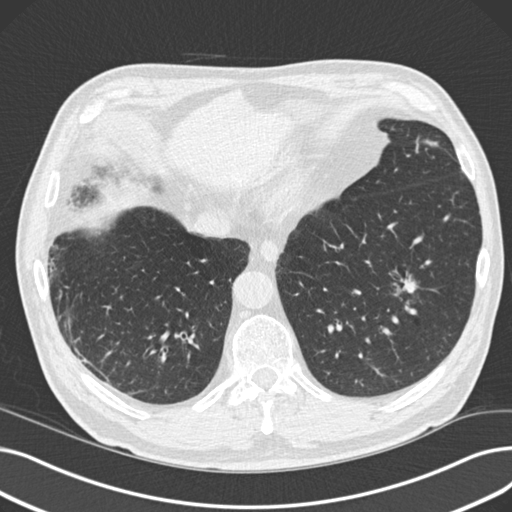
Low-dose screening chest CT, one axial slice; position 37 of 165 along the scan axis; lung window (W 1500 / L -600 HU); 2 mm slice thickness; 512 × 512 image matrix, field of view 369 × 369 mm.
Outlined on this slice (outlined manually by an expert reader):
- lesion 1 (tumor, lower lobe of left lung): box from (x=401, y=279) to (x=417, y=294) px